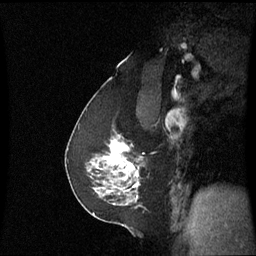
Breast MRI (dynamic contrast-enhanced), one sagittal slice; position 39 of 60 along the scan axis; dynamic contrast-enhanced series, image 2 of 3 at this slice position (ordered by acquisition); 1.5 T; TE 4.2 ms, TR 8.9 ms; 256 × 256 image matrix. Female patient, age 58 years. From the clinical record (not read from this slice): setting: breast cancer imaged before/during neoadjuvant chemotherapy; receptor status: triple-negative.
Annotated regions visible in this slice (semi-automatic segmentation, software-assisted and operator-edited):
- analysis volume of interest (the breast-tissue region the enhancement analysis was run in; not a lesion): bounding box <90,136,141,193> (left, top, right, bottom; pixels)
- tumour enhancement mask (voxels above the 70 % enhancement threshold inside the analysis volume of interest): <104,140,139,187>